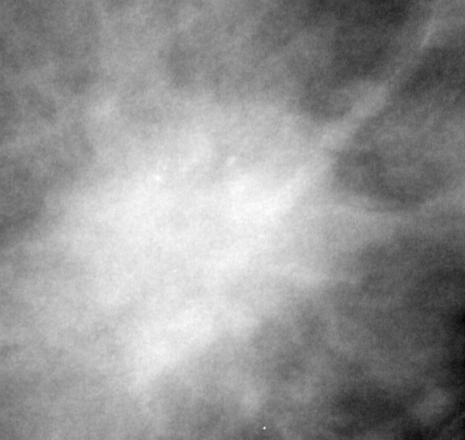
Crop from a digitized film mammogram around one marked abnormality; right breast; CC view.
- Marked abnormality: mass, shape irregular, margins spiculated; BI-RADS assessment category 5; subtlety rating 3 on a 1 (subtle) to 5 (obvious) scale; pathology result (as recorded, not read from the image): malignant.